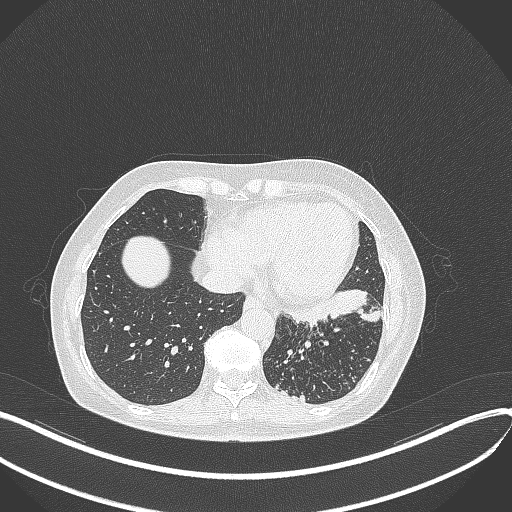
Chest CT, one axial slice; slice 122 of 429 in the series (ordered by position); reconstruction kernel B70f; 100 kVp; lung window (W 1500 / L -600 HU); 1 mm slice thickness; 512 × 512 image matrix. Patient: female, 63 years. From the clinical record (not read from this slice): clinical TNM (as recorded): T1b N0 M0; histopathological grade: G2-3.
Annotated regions visible in this slice (rectangle marked by the reading radiologist):
- lung tumour (recorded histology: adenocarcinoma): bounding box <286,288,381,330> (left, top, right, bottom; pixels)